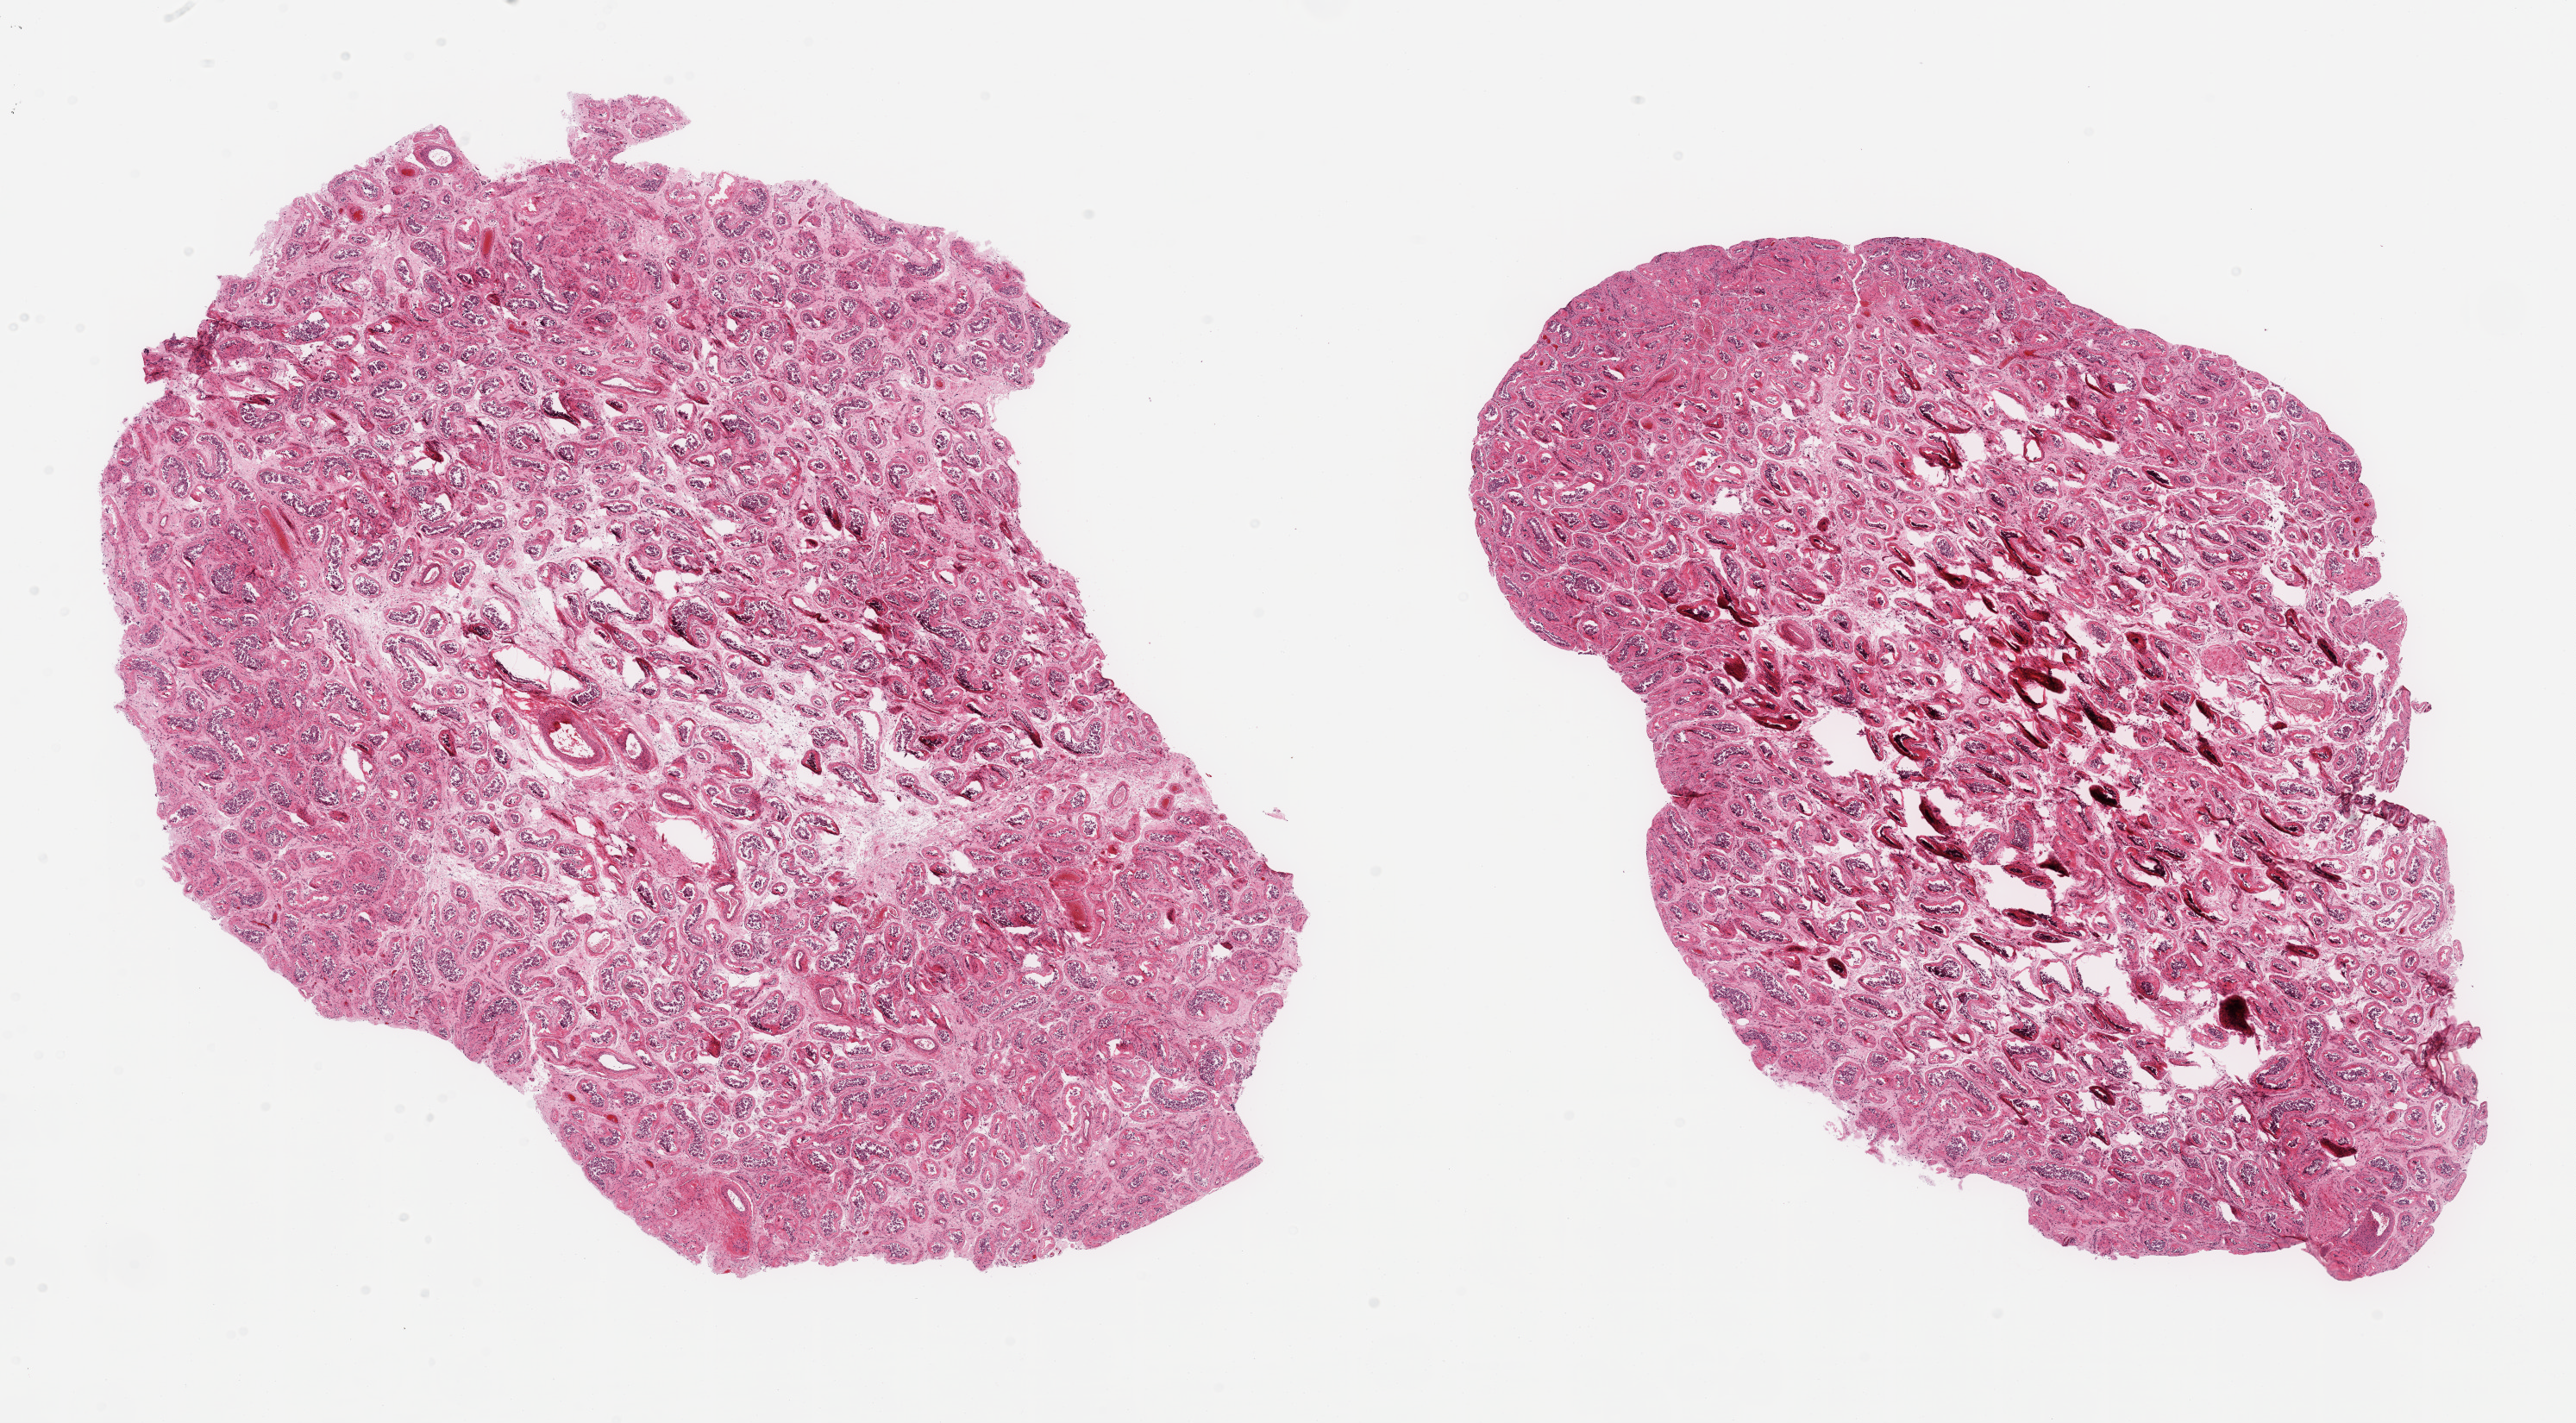
Digitized haematoxylin and eosin-stained section, brightfield, low-resolution overview of the scanned area, about 23.6 x 13.1 mm; PAXgene-fixed paraffin-embedded (PFPE) section; section of testis (target tissue); tissue donor sample.
• reviewer comment on this tissue sample: 2 pieces, tubular atrophy with markedly reduced spermatogenesis